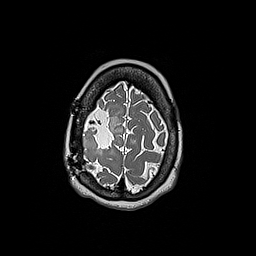
Brain MRI from a brain-tumour surgery series, one axial slice; position 46 of 192 along the scan axis; 1 mm slice thickness; 256 × 256 image matrix, field of view 250 × 250 mm. Case-level facts recorded for this patient, not image findings: histopathology: Oligodendroglioma; WHO grade: 3; IDH mutation: yes; tumour location: Right Frontal.
Structures marked on this image (outlined manually by an expert reader):
- tumour: bounding box (x1, y1, x2, y2) in pixels: (82, 129, 98, 151)